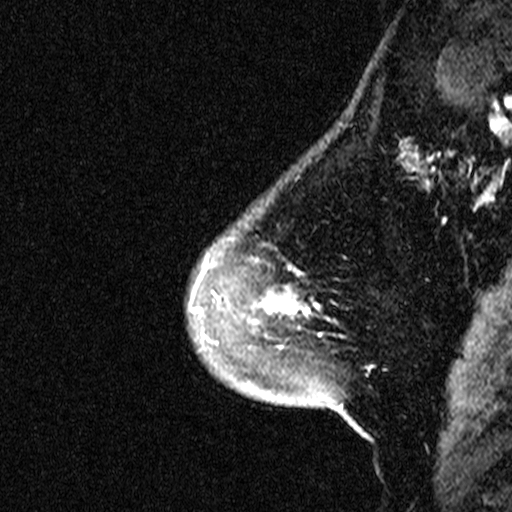
Breast MRI (dynamic contrast-enhanced), one sagittal slice. Slice 8 of 44 in the series (ordered by position). Dynamic contrast-enhanced study with each time point stored as its own series, time point 2 of 3 at this slice position (early post-contrast, ordered by acquisition time). 1.5 T. TE 4.5 ms, TR 11 ms. 3 mm slice thickness. 512 × 512 image matrix, field of view 200 × 200 mm. Female patient, age 46 years. From the clinical record (not read from this slice): setting: breast cancer imaged before/during neoadjuvant chemotherapy; receptor status: HER2-positive.
Structures marked on this image (semi-automatically segmented with operator editing):
- analysis volume of interest (the breast-tissue region the enhancement analysis was run in; not a lesion): bounding box <191,172,359,393> (left, top, right, bottom; pixels)
- tumour enhancement mask (voxels above the 90 % enhancement threshold inside the analysis volume of interest): <259,270,311,348>